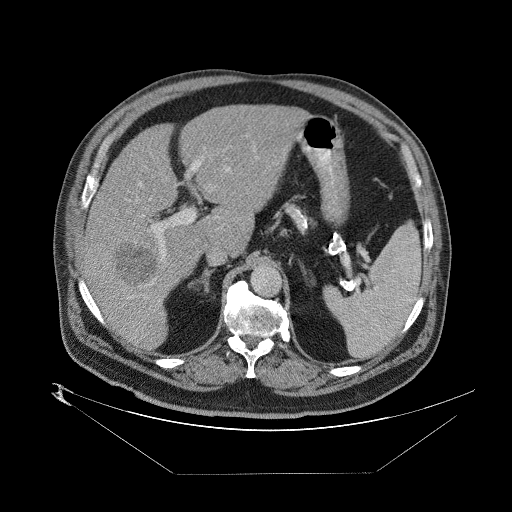
Contrast-enhanced abdominal CT (liver protocol), one axial slice; slice 50 of 89 in the series (ordered by position); 140 kVp; one of 2 acquisitions stored at this slice position; soft-tissue window (W 400 / L 40 HU); 2.5 mm slice thickness; 512 × 512 image matrix, field of view 480 × 480 mm. Case-level facts recorded for this patient, not image findings: diagnosis: hepatocellular carcinoma (patient treated with transarterial chemoembolisation; whether this scan precedes or follows treatment is not stated here); TNM stage (as recorded): Stage-II; Child-Pugh class: B; tumour differentiation: moderately differentiated.
Structures marked on this image (semi-automatic segmentation, software-assisted and operator-edited):
- abdominal aorta: bounding box [x1, y1, x2, y2] px = [252, 266, 281, 295]
- liver parenchyma outside the tumour (the mass and vessels are separate outlines, so this box may not span the whole liver): [82, 101, 304, 348]
- mass: [108, 235, 156, 287]
- liver vessels: [87, 132, 282, 320]